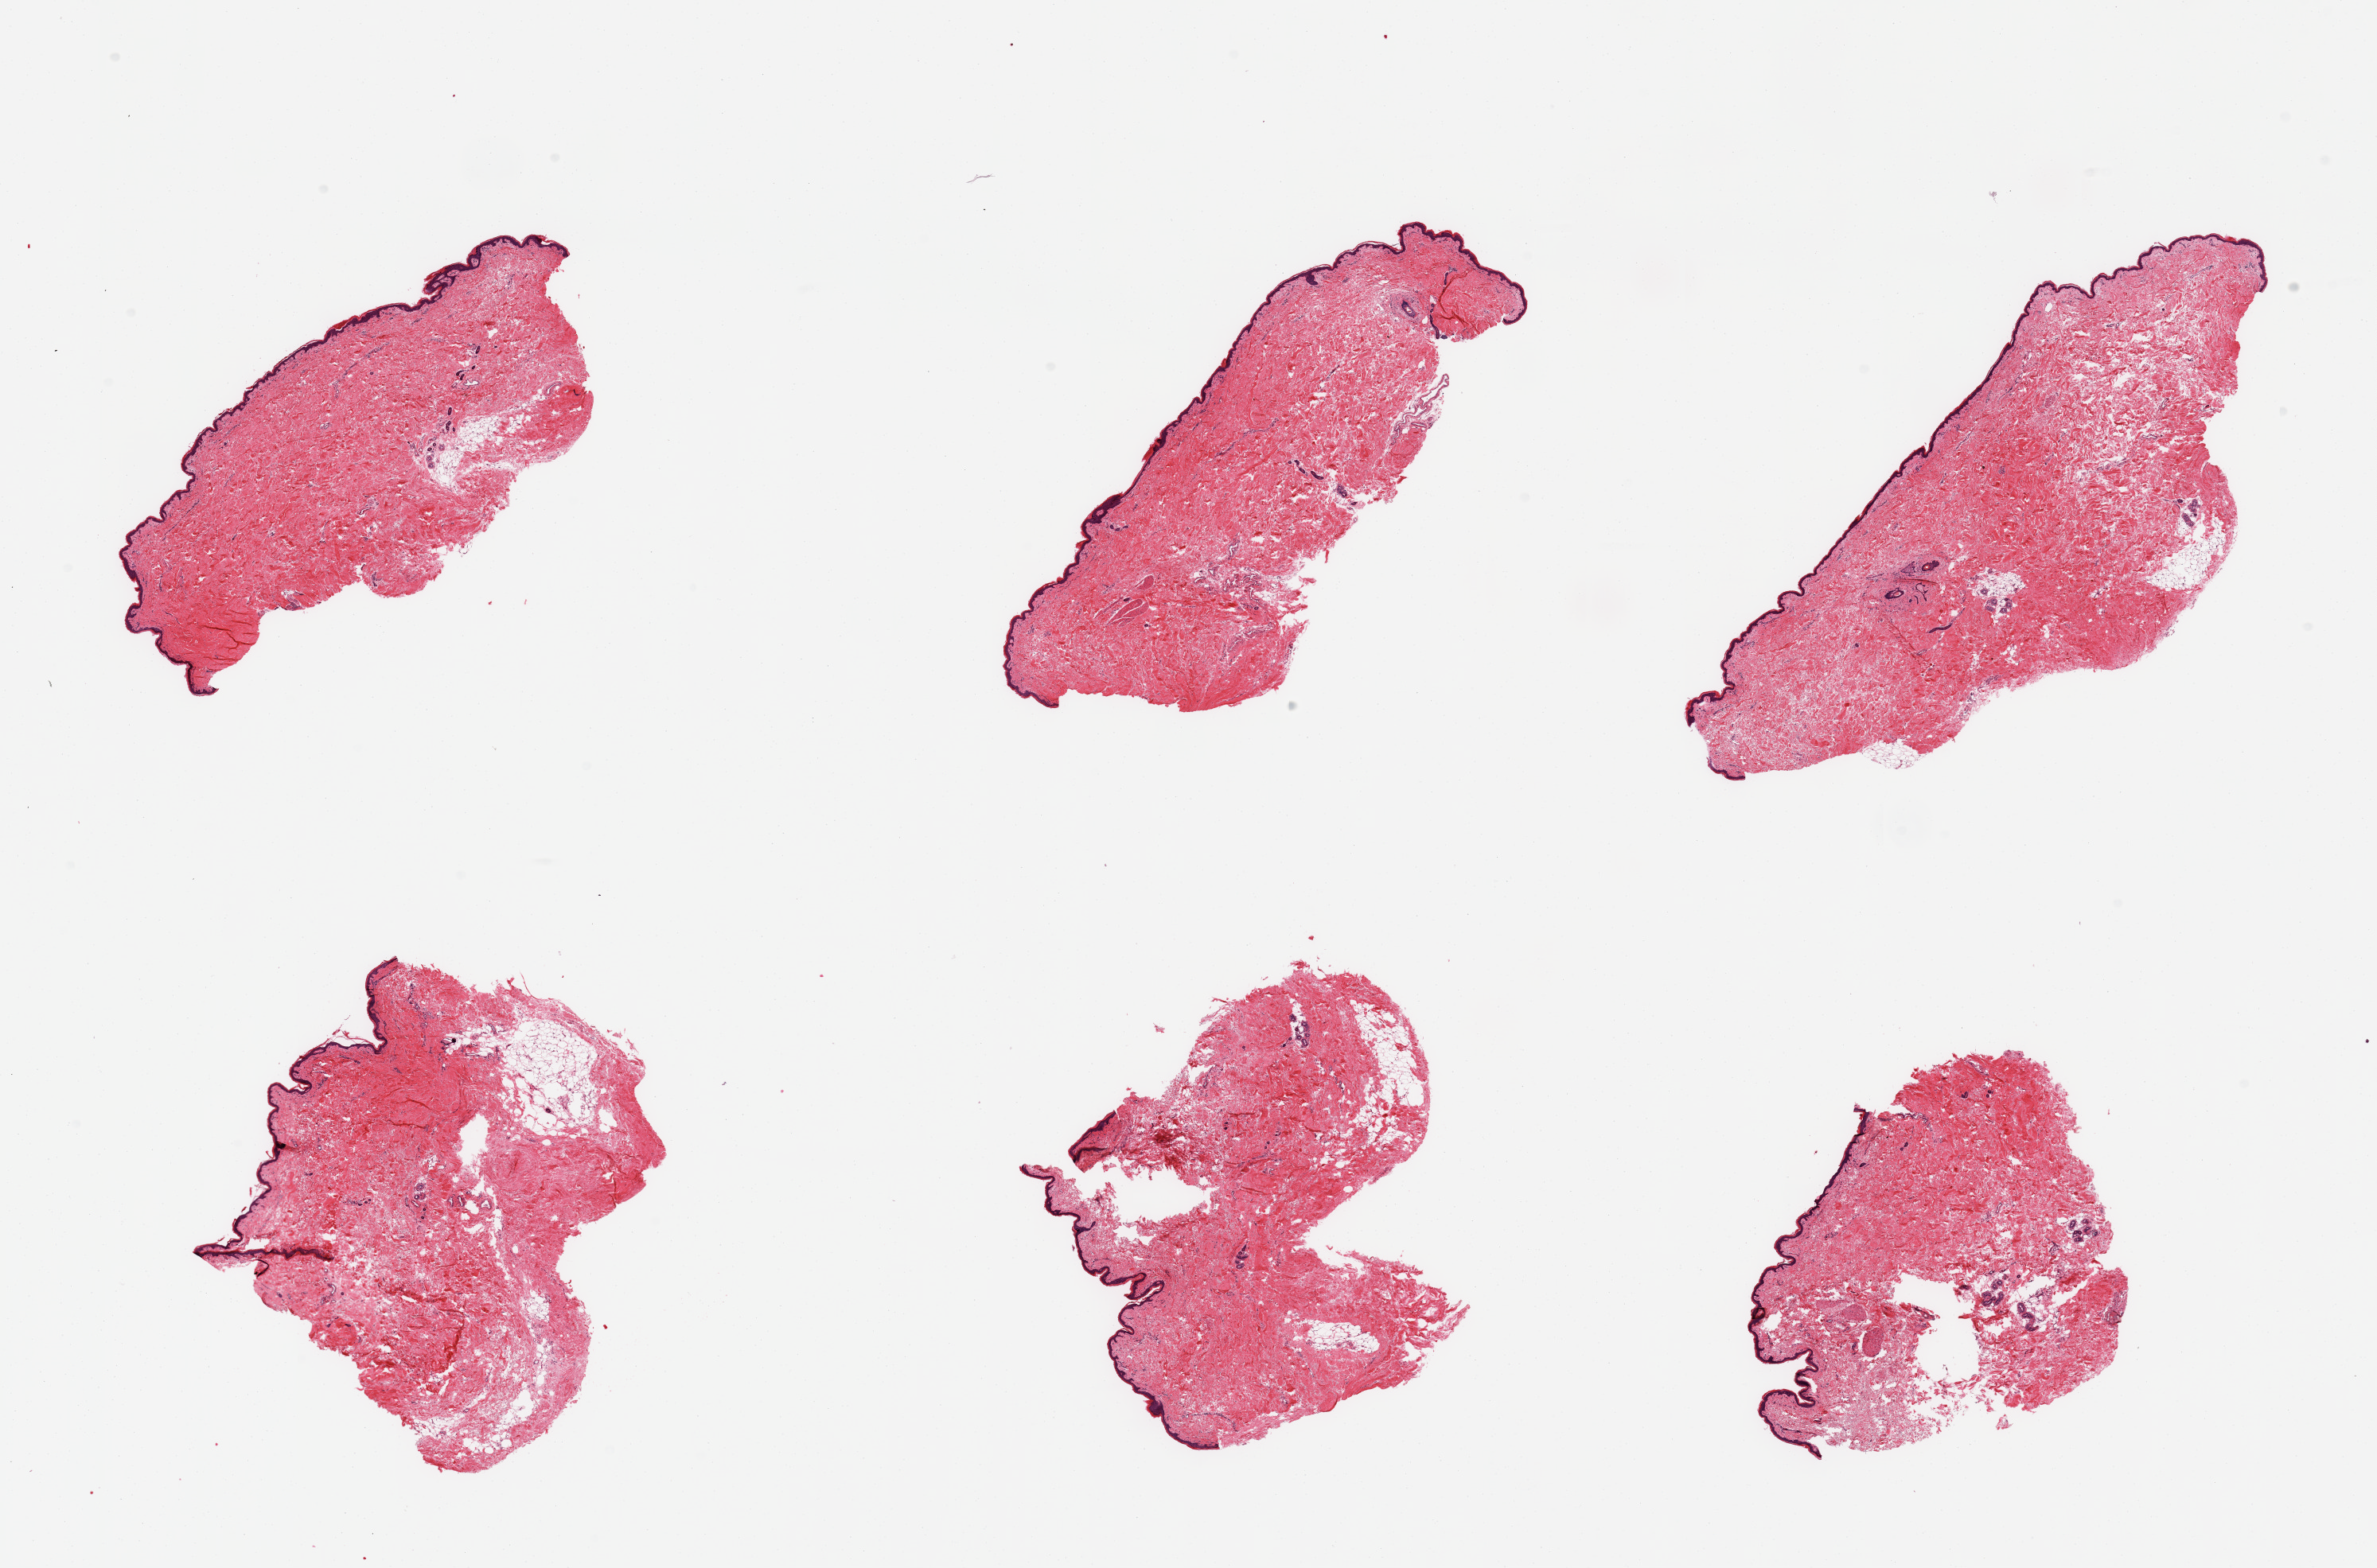
Digitized haematoxylin and eosin-stained section, low-resolution overview of the scanned area, about 23.6 x 15.6 mm (acquisition: 20x scan). PAXgene-fixed, paraffin-embedded tissue. Target tissue: skin of suprapubic region. Donor tissue sample. Donor sex: female.
* pathologist's review note for this sample: 6 pieces; hair-free; 10% deep dermal fat